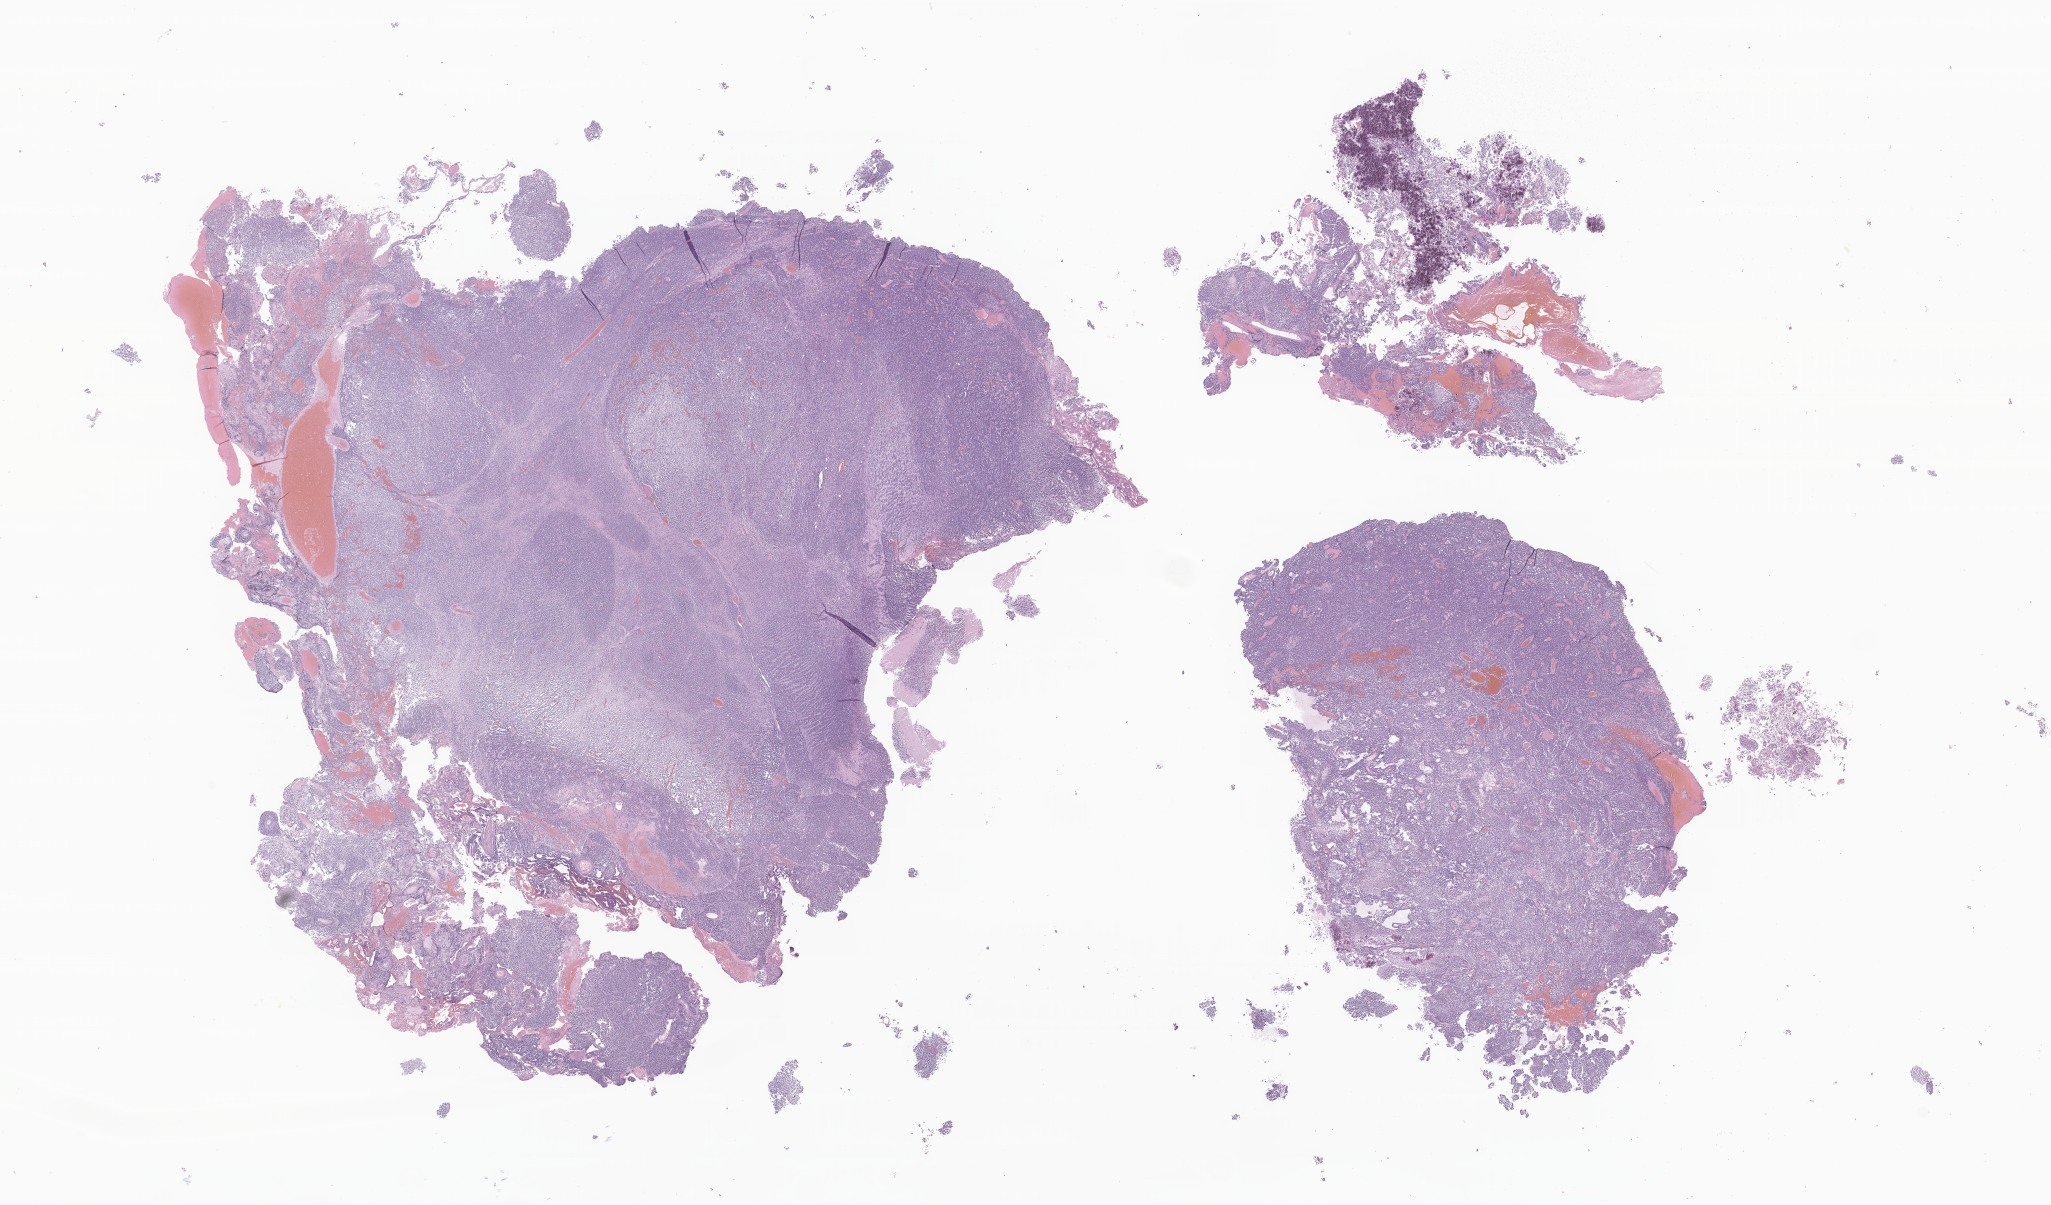
Whole-slide image, haematoxylin and eosin stain of tumor tissue from the cerebellum, a low-resolution overview of the entire scanned area, about 34.6 x 20.3 mm. Formalin-fixed, paraffin-embedded (FFPE) tissue. Patient: male, age 102 months (8 years 6 months).
Diagnosis: Medulloblastoma, NOS.